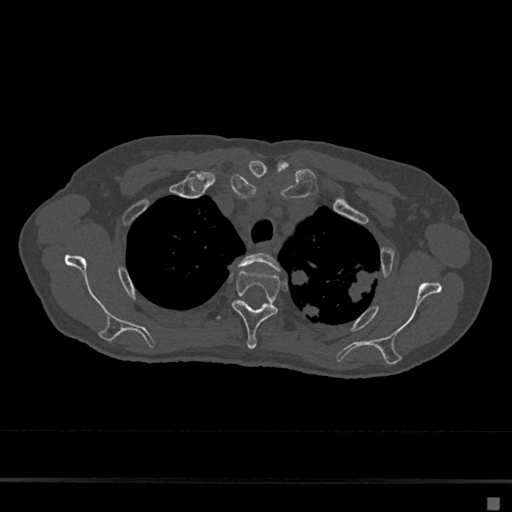
CT including the spine, one axial slice. Reconstruction kernel Br40s/3. 120 kVp. Bone window (W 1800 / L 400 HU). 0.5 mm slice thickness. 512 × 512 image matrix. Female patient, age 68 years. From the clinical record (not read from this slice): primary cancer: renal.
Outlined on this slice (semi-automatic segmentation, software-assisted and operator-edited):
- T2 vertebra: bounding box <238,253,280,303> (left, top, right, bottom; pixels)
- T3 vertebra: <232,270,280,350>
- T4 vertebra: <216,315,221,321>